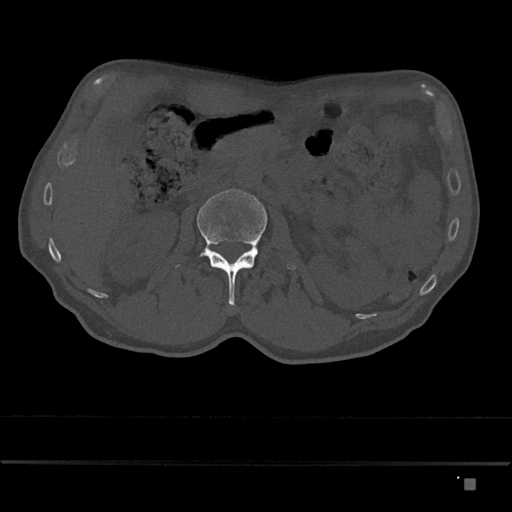
CT including the spine, one axial slice; slice 474 of 797 in the series (ordered by position); reconstruction kernel Br40s/3; 120 kVp; bone window (W 1800 / L 400 HU); 0.5 mm slice thickness; 512 × 512 image matrix, field of view 390 × 390 mm. Patient: male, 72 years. Case-level facts recorded for this patient, not image findings: primary cancer: prostate.
Outlined on this slice (semi-automatically segmented with operator editing):
- L2 vertebra: bounding box <176,189,296,306> (left, top, right, bottom; pixels)